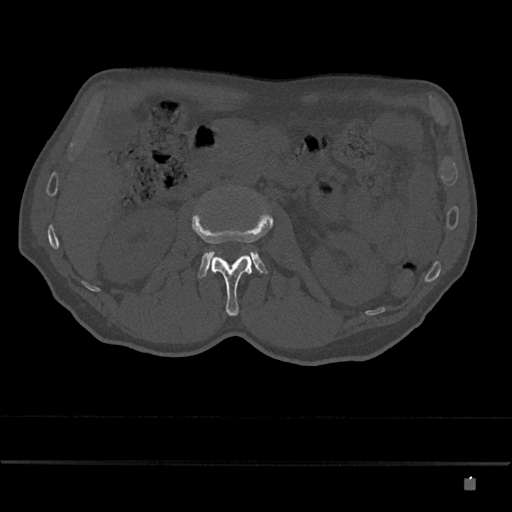
CT including the spine, one axial slice; reconstruction kernel Br40s/3; 120 kVp; bone window (W 1800 / L 400 HU); 0.5 mm slice thickness; 512 × 512 image matrix, field of view 390 × 390 mm. Patient: male, 72 years. Case-level facts recorded for this patient, not image findings: primary cancer: prostate.
Structures marked on this image (semi-automatic segmentation, software-assisted and operator-edited):
- L2 vertebra: bounding box [x1, y1, x2, y2] px = [192, 210, 274, 316]
- L3 vertebra: [198, 251, 267, 278]